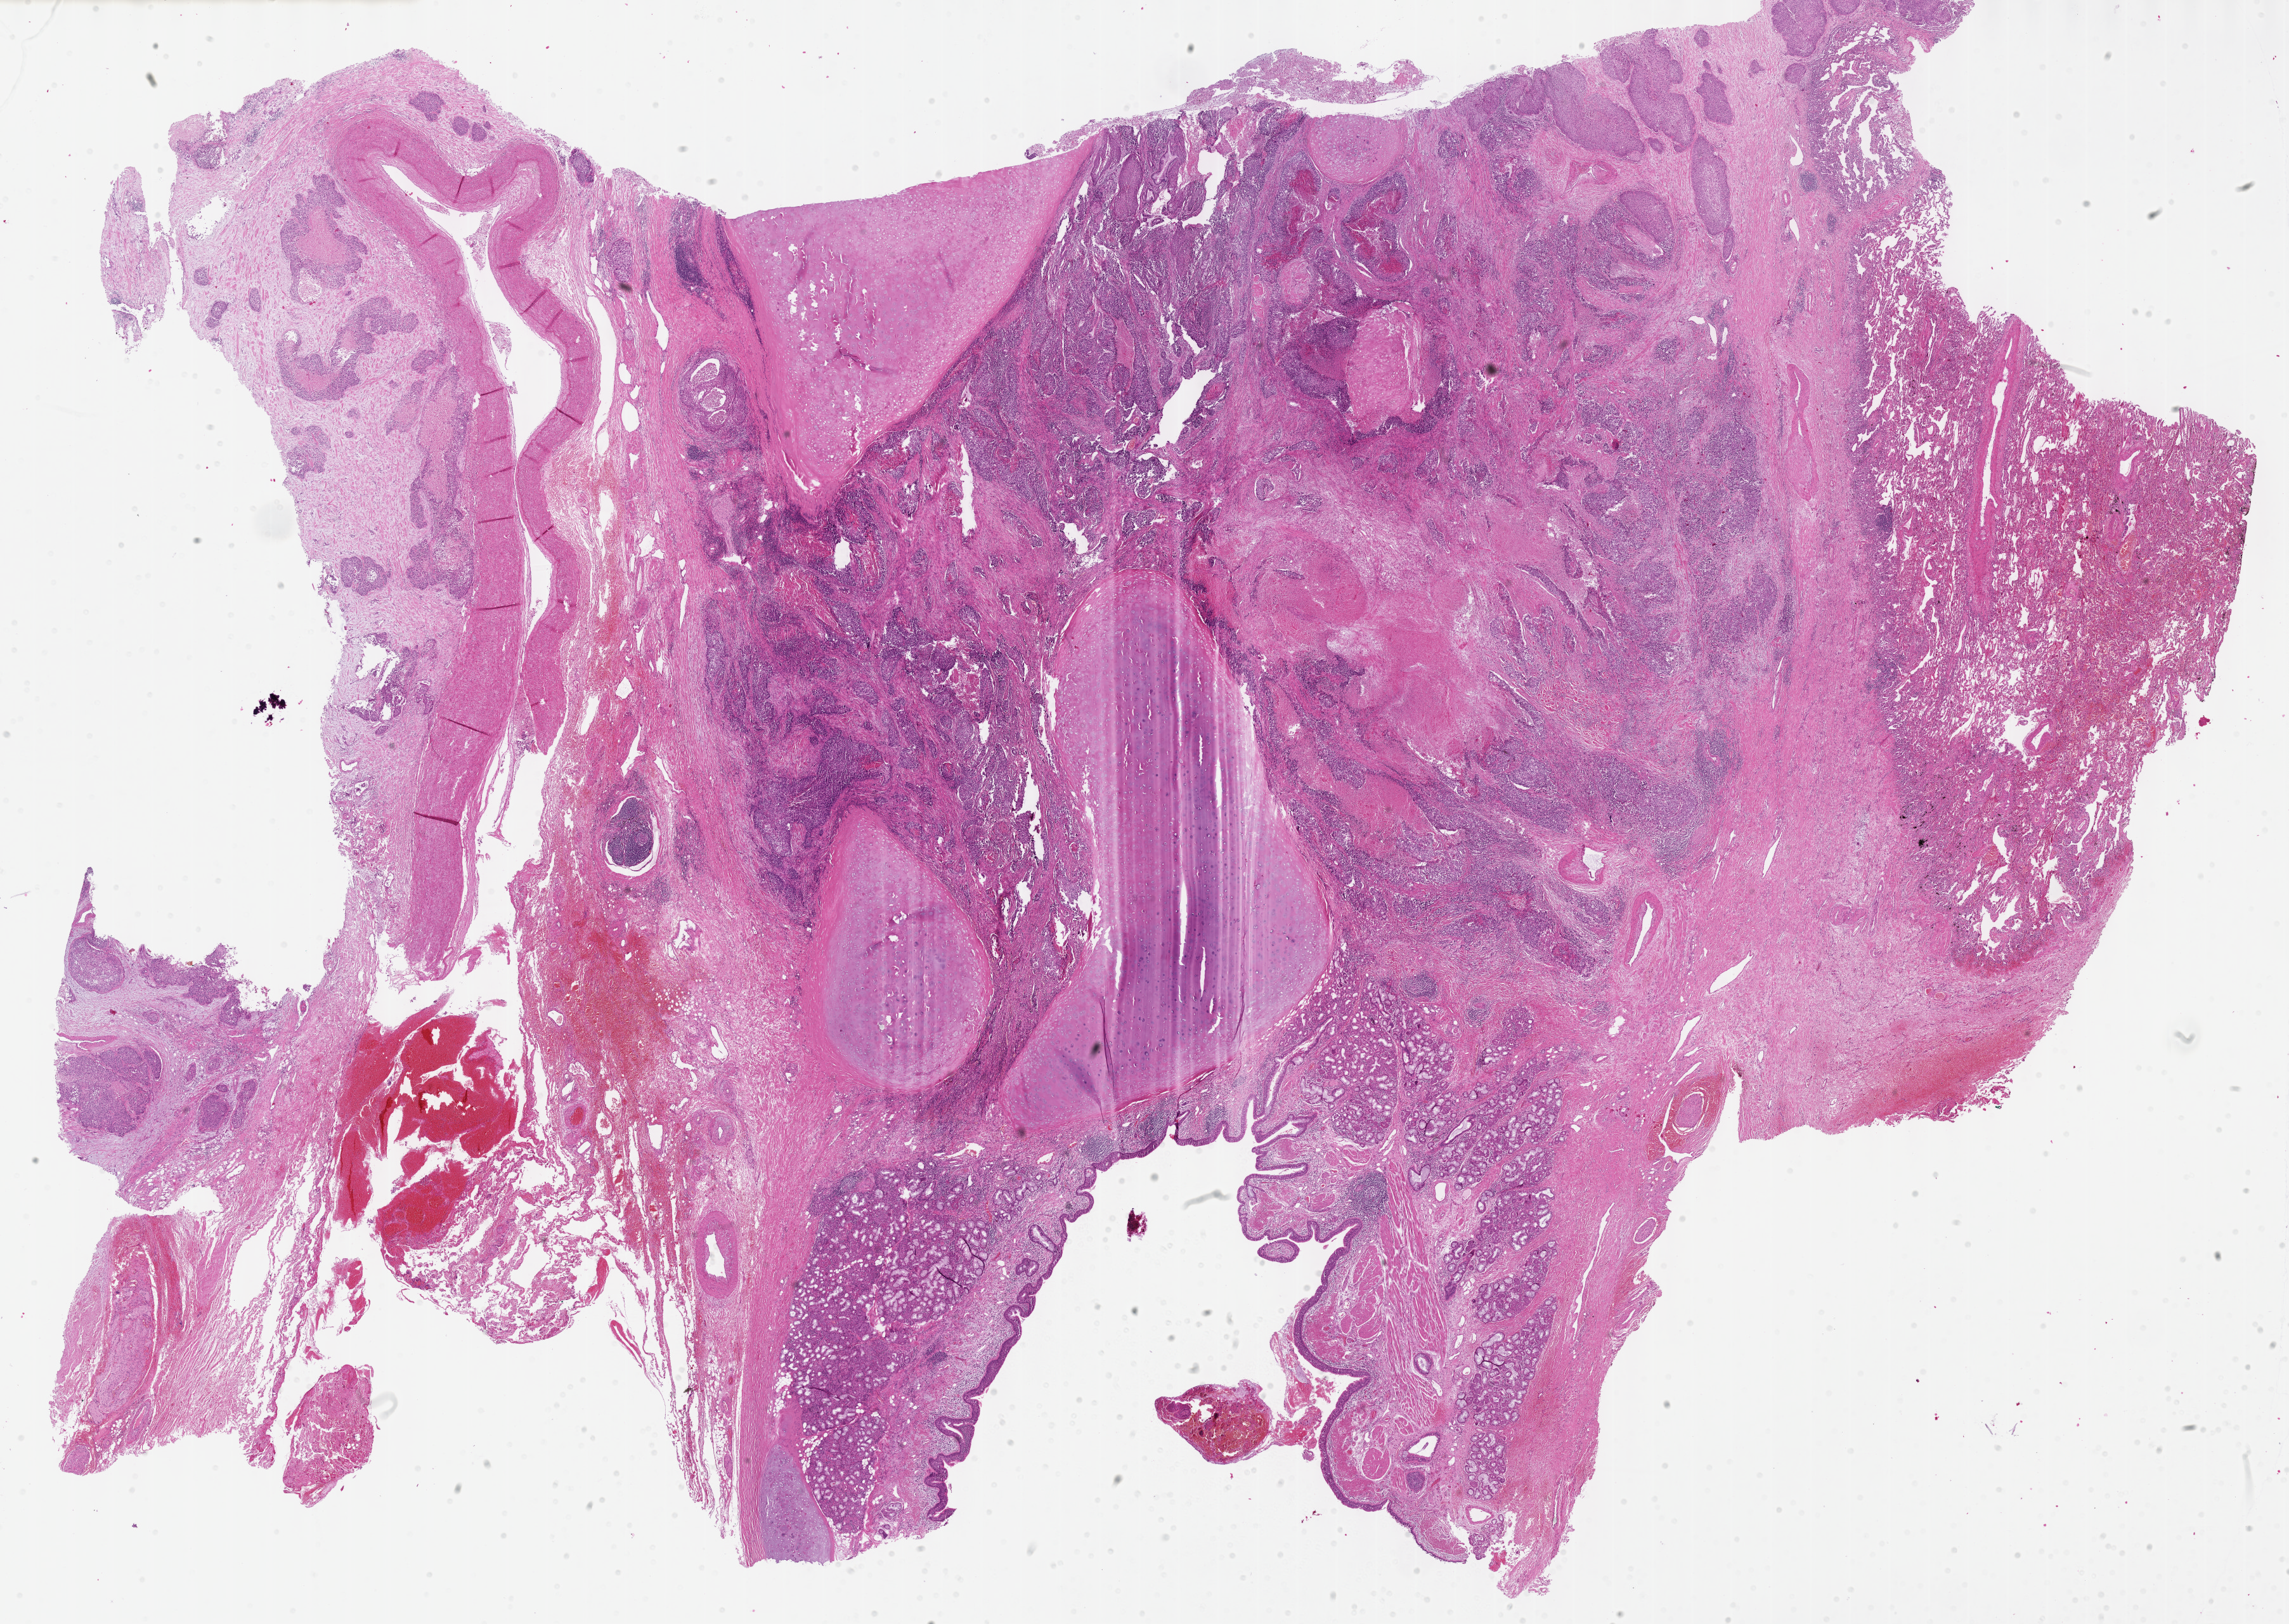
H&E whole-slide image — shown as a low-resolution overview of the whole scanned area (about 29.2 x 20.7 mm). Formalin-fixed paraffin-embedded (FFPE) diagnostic section. Sample: primary tumour, lung. Male patient; age at initial diagnosis 69 years.
Laterality: right. Histologic diagnosis: Squamous cell carcinoma, NOS (overlapping lesion of lung). AJCC pathologic stage: IIIA.